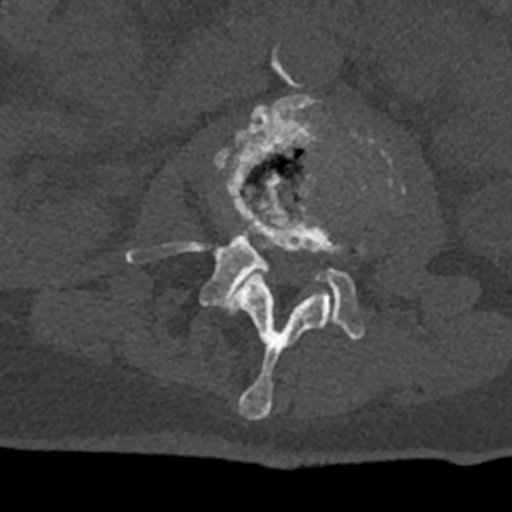
CT including the spine, one axial slice; position 349 of 797 along the scan axis; reconstruction kernel Br40s/3; 120 kVp; bone window (W 1800 / L 400 HU); 0.5 mm slice thickness; 512 × 512 image matrix, field of view 160 × 160 mm. Male patient, age 74 years. Case-level facts recorded for this patient, not image findings: primary cancer: renal; vertebrae with lytic lesions (as recorded): T10, L1, L2, L3, L4, L5.
Outlined on this slice (semi-automatic segmentation, software-assisted and operator-edited):
- L2 vertebra: bounding box [x1, y1, x2, y2] px = [230, 154, 365, 420]
- L3 vertebra: [126, 94, 400, 340]